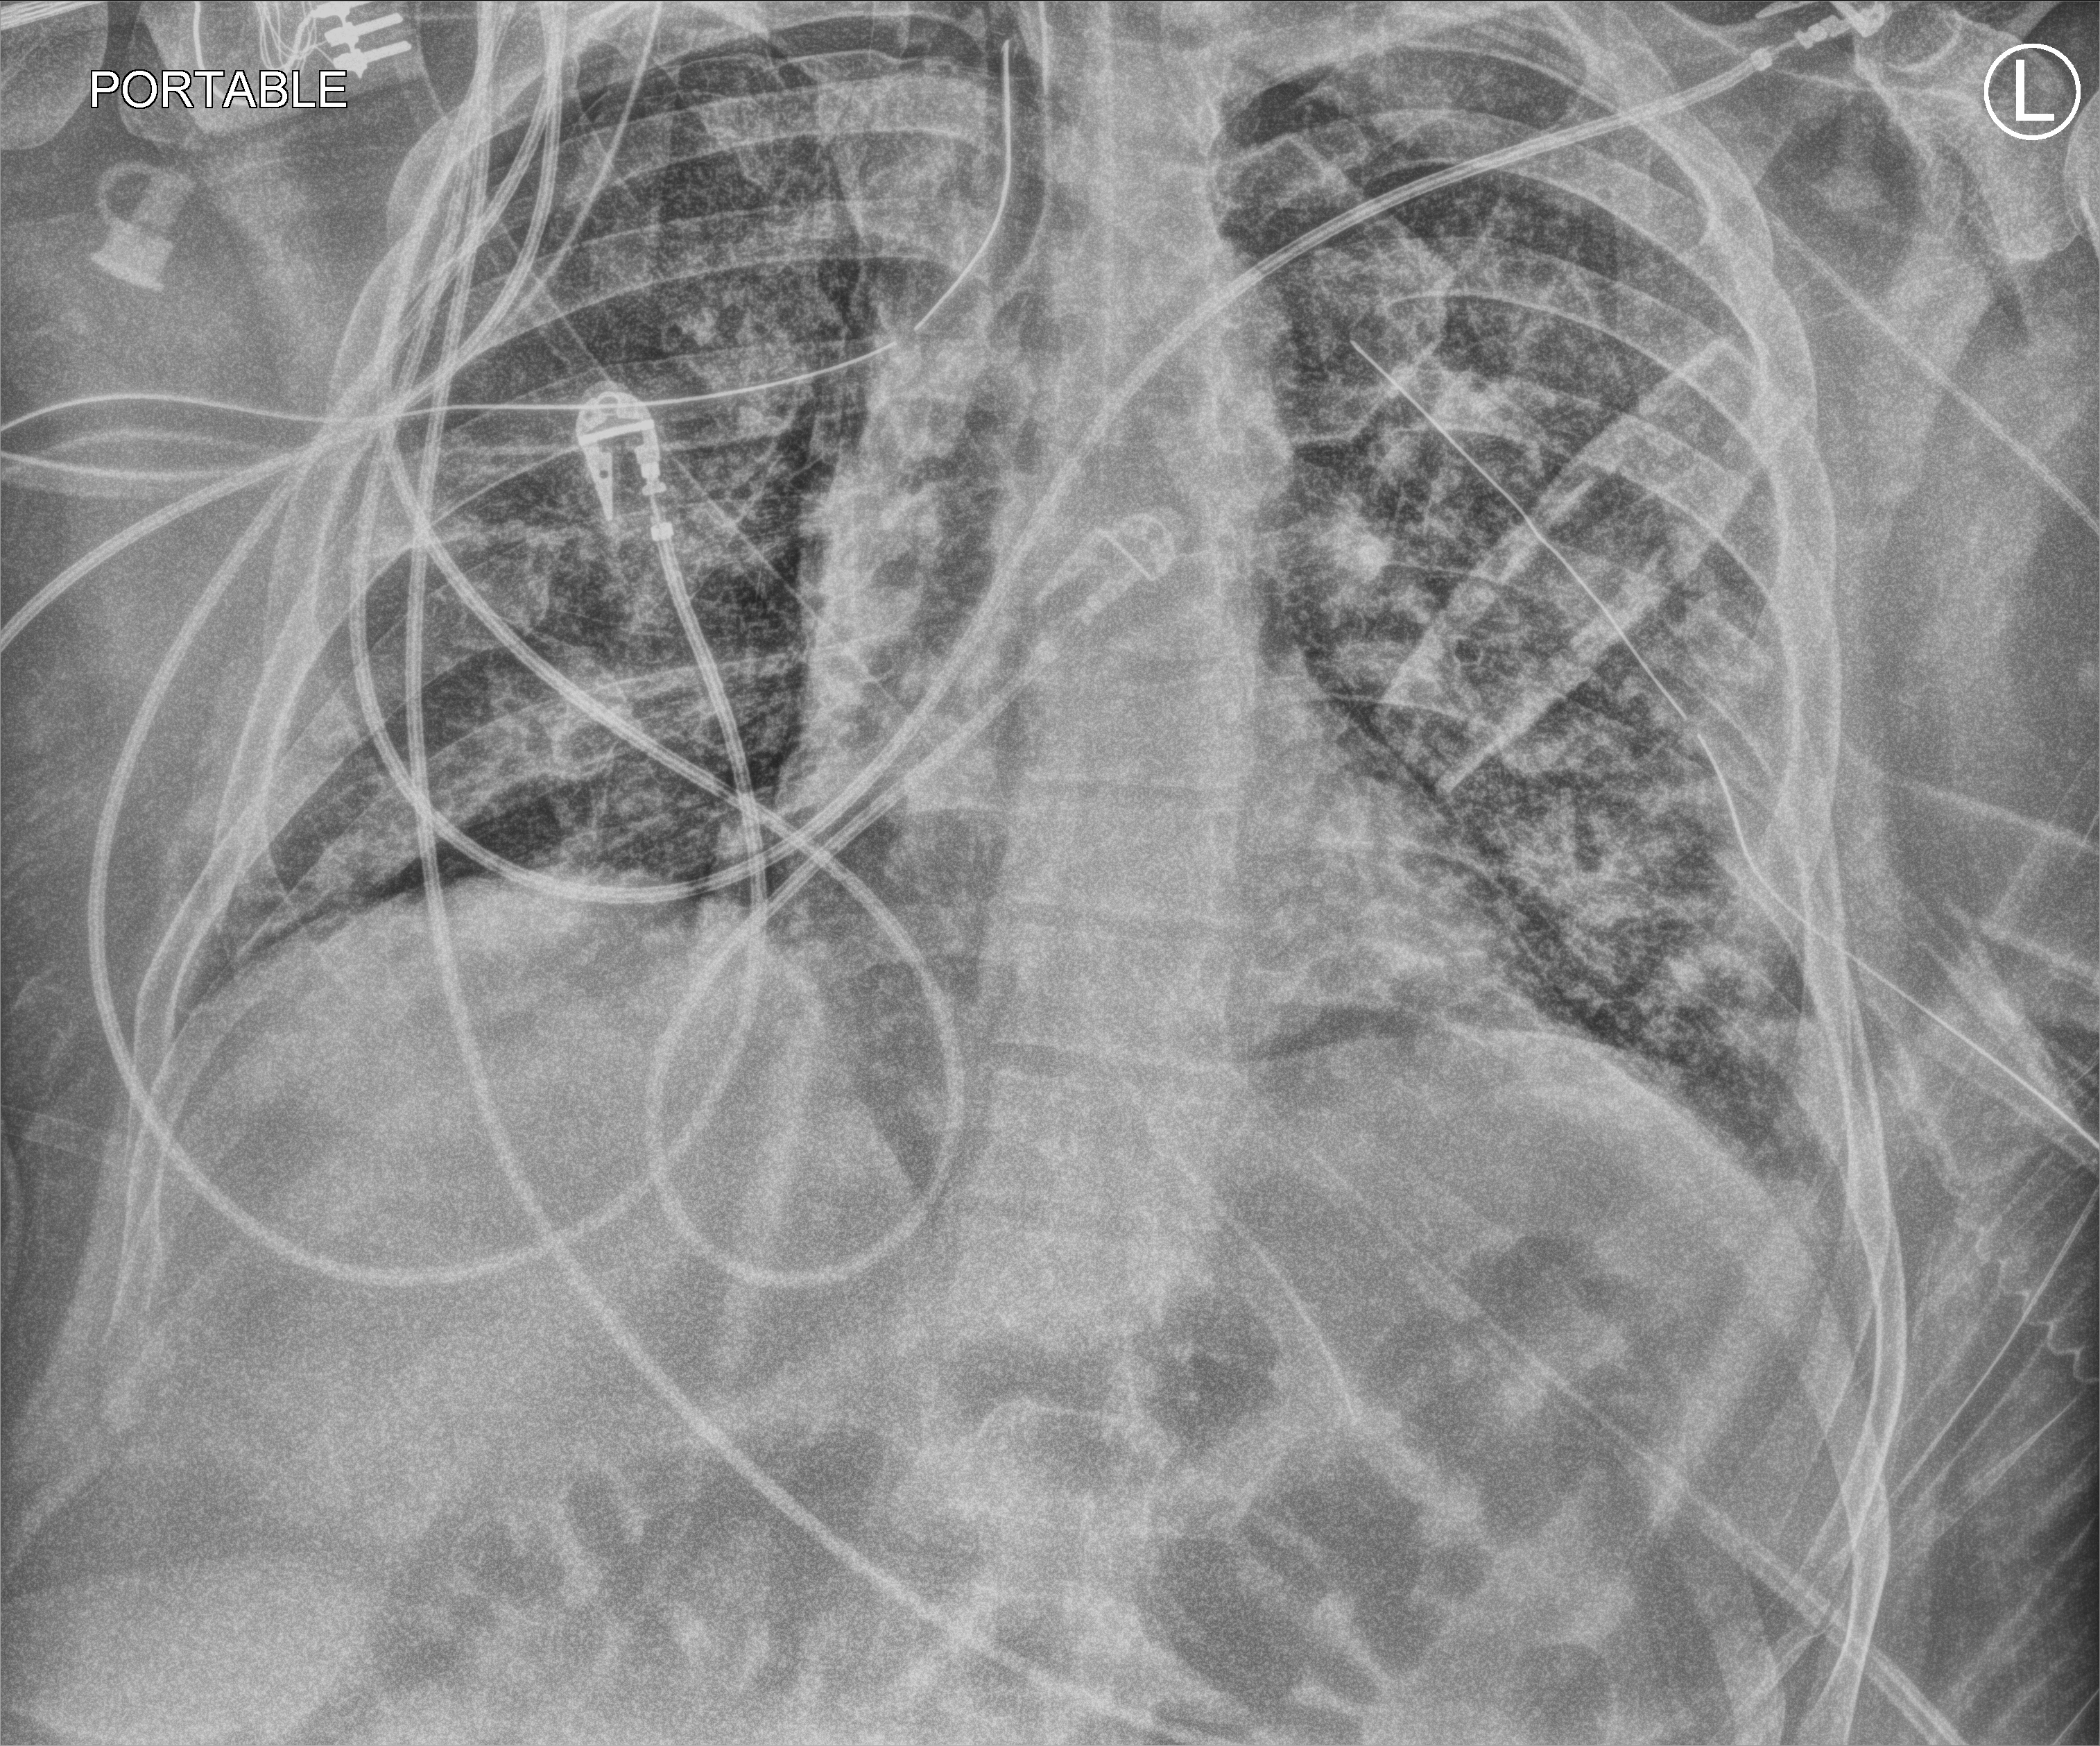
Chest X-ray (portable), anteroposterior (AP) projection. Male patient hospitalised with COVID-19, age 18–59 years.
From the hospital-stay record, not from the radiograph (when in the stay this image was taken is not recorded): other chronic lung disease (admission record): no; length of hospital stay: 63 days.